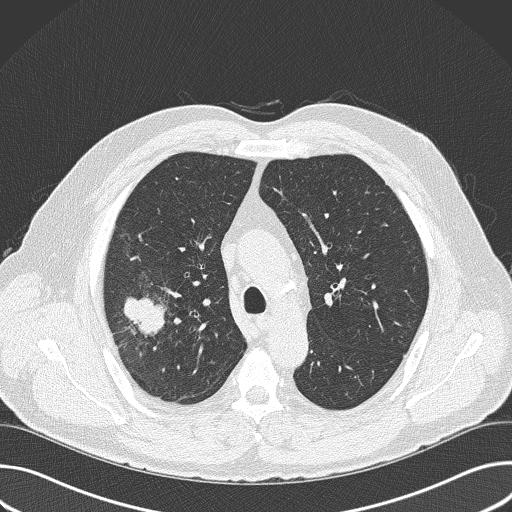
Chest CT (low-dose screening protocol), one axial image. Baseline annual screen. Lung window (W 1500 / L -600 HU). 2 mm slice thickness. Slice 114 of 157 in the series. 512 × 512 image matrix, field of view 380 × 380 mm. Male, age 56 years at enrolment. Current smoker at enrolment.
Expert reader's lesion annotation, box from (x=84, y=269) to (x=190, y=380) px. Reader record for this screening exam (exam-level; its link to the box is not recorded): non-calcified nodule or mass ≥4 mm, right upper lobe, 6 × 5 mm, spiculated (stellate) margins, soft tissue attenuation.